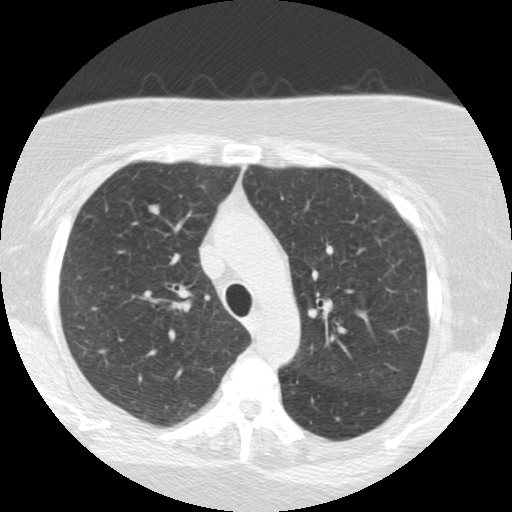
Axial slice from a low-dose chest CT screening exam, second screening round (one year after baseline), lung window (W 1500 / L -600 HU), standard (soft-tissue) reconstruction kernel (STANDARD), slice 168 of 225 in the series, 512 × 512 image matrix, field of view 320 × 320 mm. Female participant, aged 64 years at enrolment. Current smoker at enrolment.
Lesion marked by an expert reader, bounding box [x1, y1, x2, y2] px = [131, 195, 170, 232]. Screening reader's record for this exam (one nodule recorded; not confirmed to be the boxed lesion): non-calcified nodule or mass ≥4 mm, right upper lobe, 8 × 7 mm, smooth margins, soft tissue attenuation, pre-existing on the prior screen: no. Official screen result: positive, other.